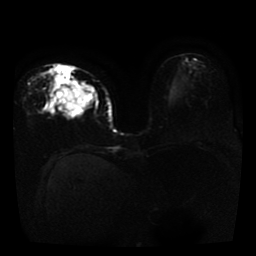
Breast MRI, one axial slice. Slice 15 of 41 in the series (ordered by position). Diffusion-weighted series; image 2 of 4 stored at this slice position (different b-values; order by instance number). 1.5 T. 5 mm slice thickness. 256 × 256 image matrix, field of view 330 × 330 mm. Female patient.
Annotated regions visible in this slice (outlined manually by an expert reader):
- tumour on diffusion-weighted imaging: box from (x=58, y=77) to (x=94, y=111) px